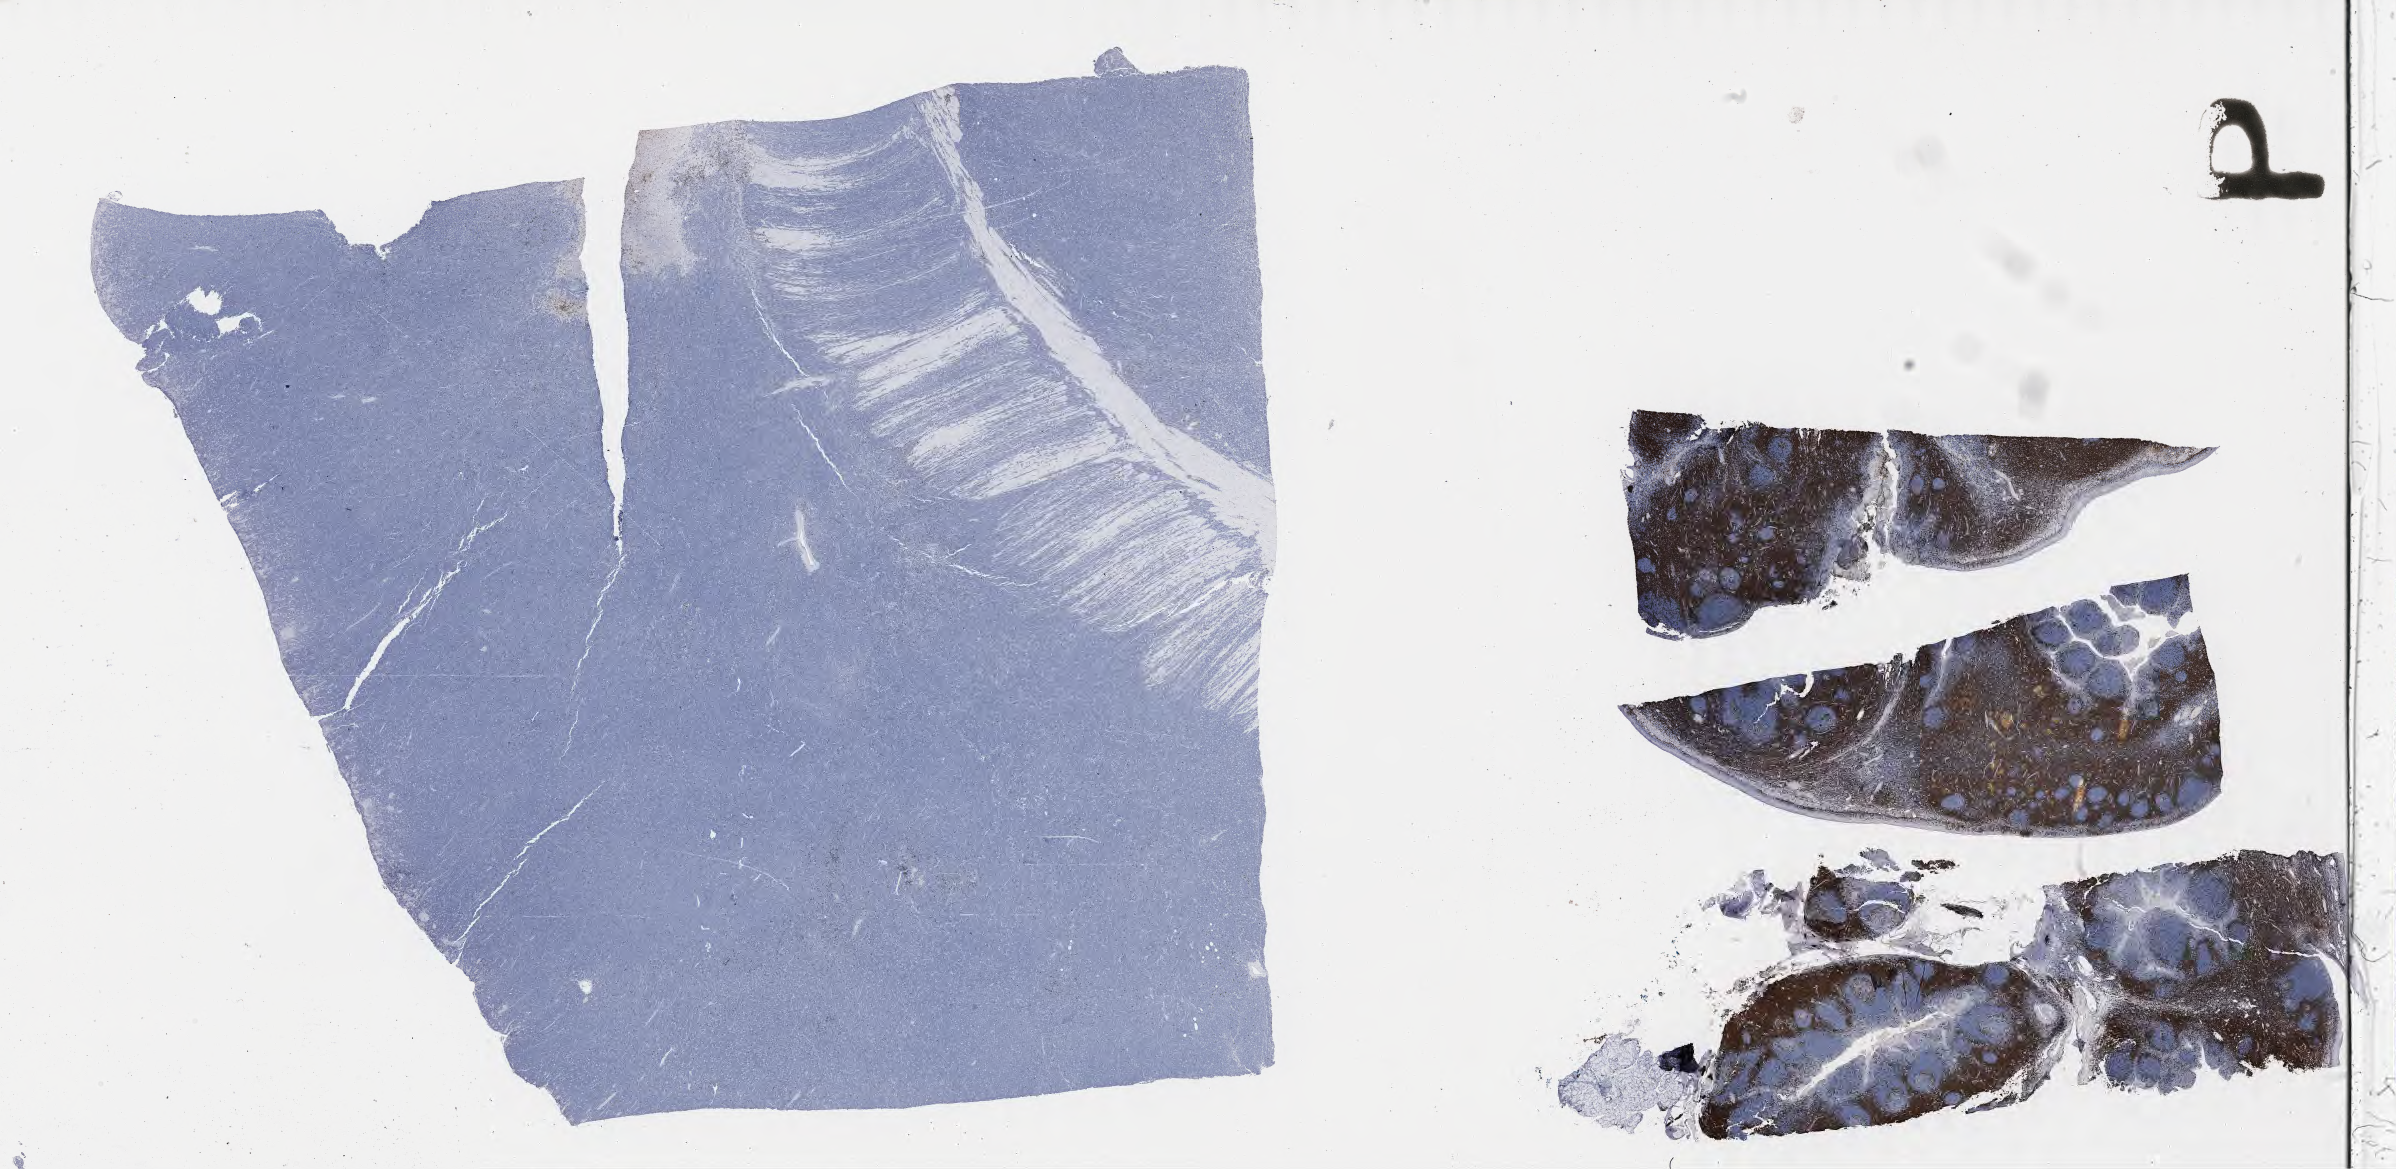
Immunohistochemistry (IHC) whole-slide image stained for CD3, a low-resolution overview of the entire scanned area, about 38.7 x 18.9 mm, specimen: tumor tissue, site: colon. Patient male; 14 years old.
• diagnosis: Burkitt lymphoma, NOS